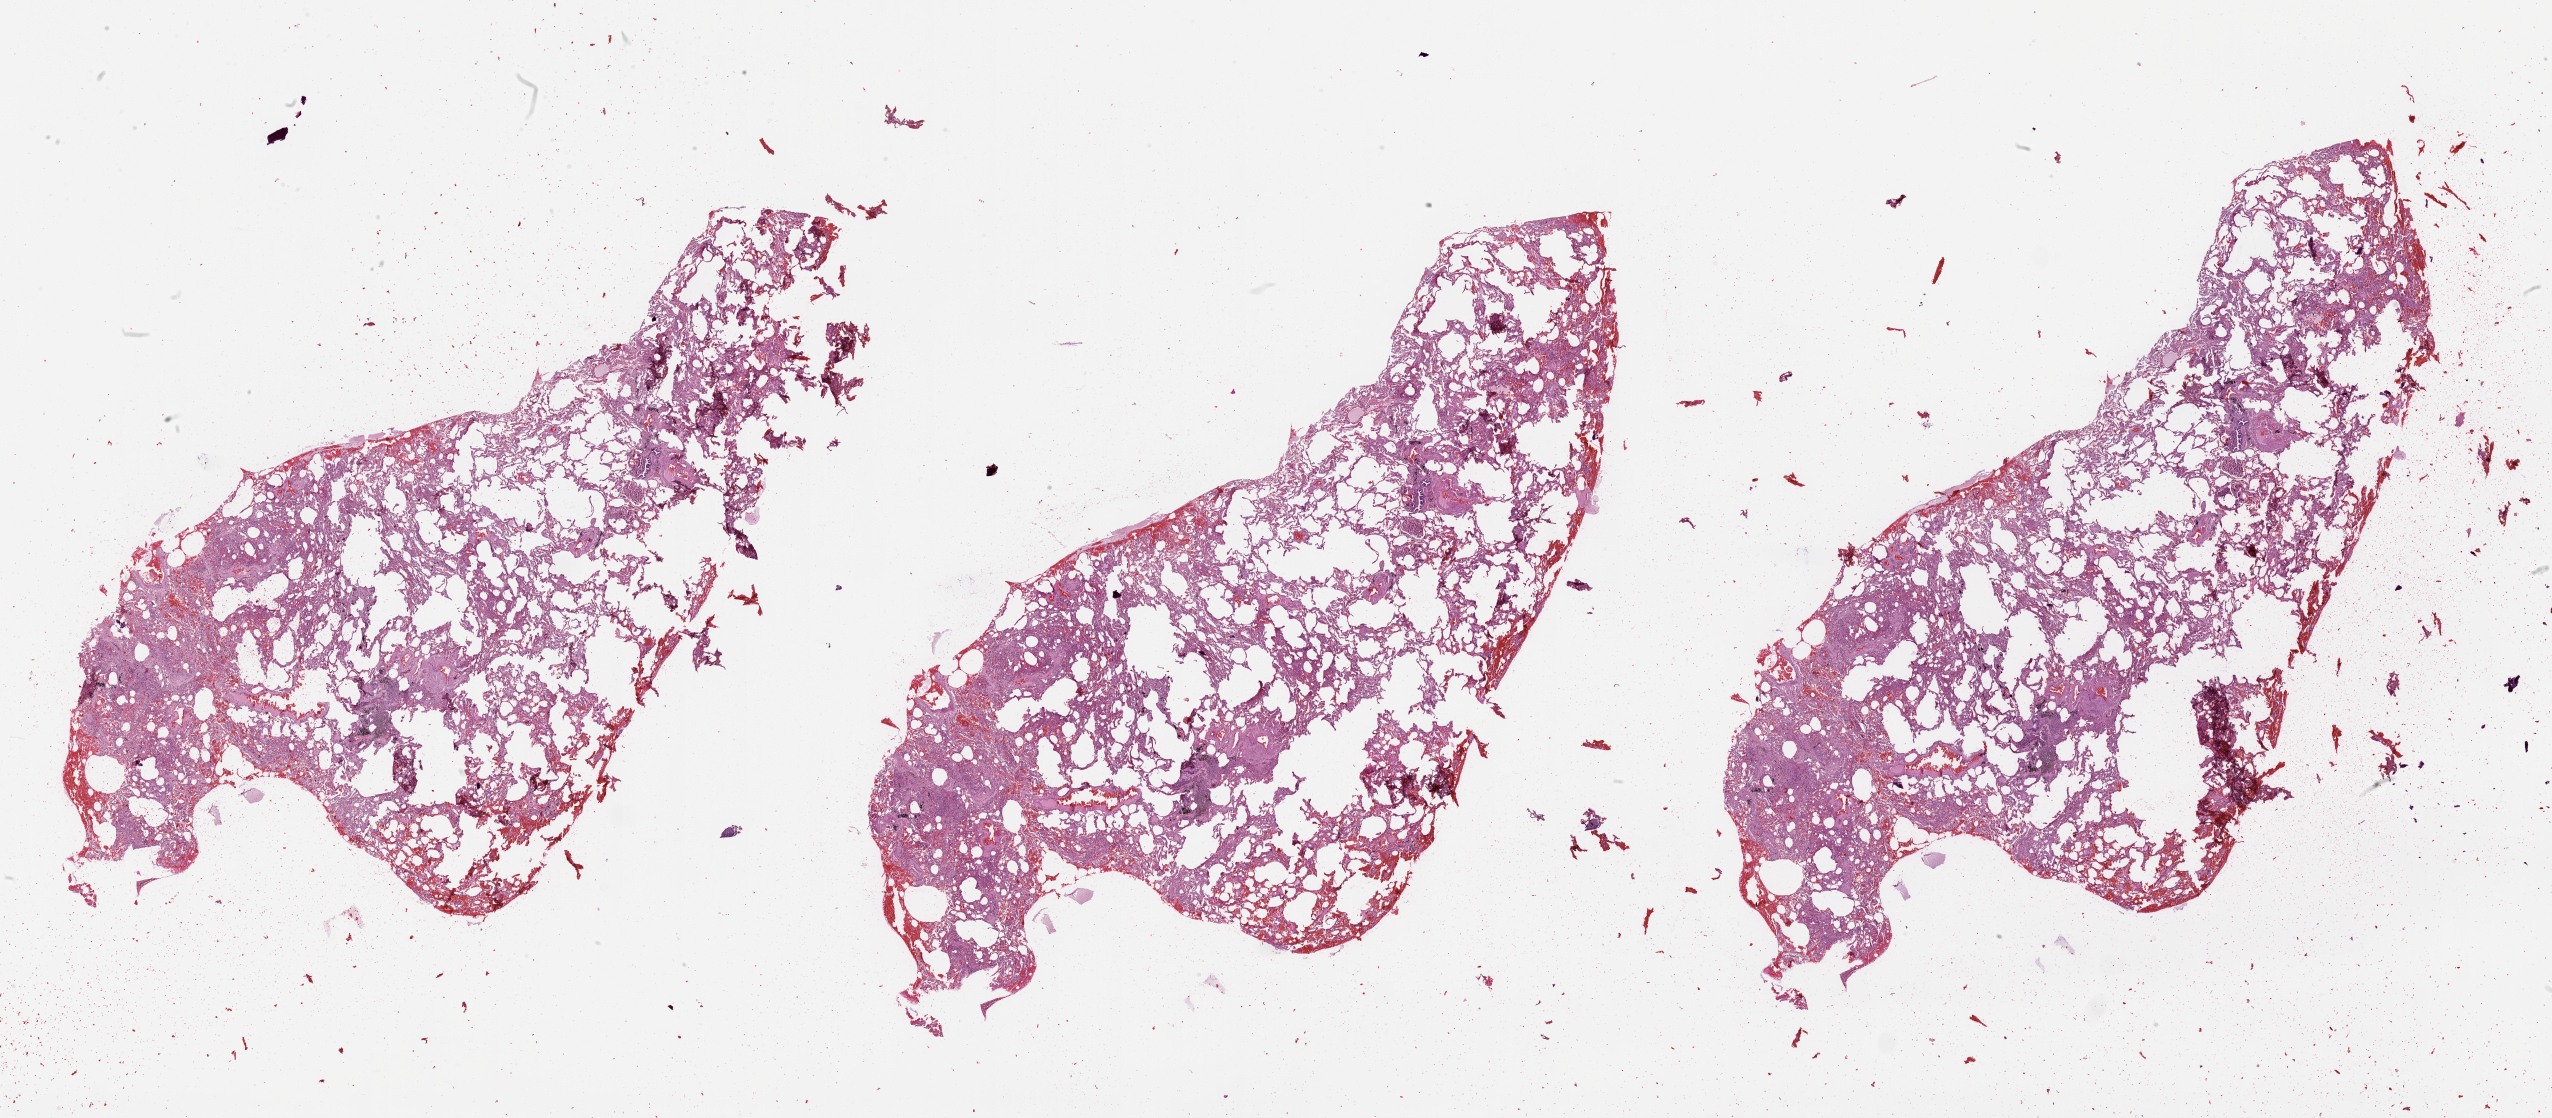
Whole-slide histology image, H&E-stained, a low-resolution overview of the entire scanned area, about 41.1 x 18.0 mm (from a 20x scan), lung, normal (non-tumour) tissue. Patient: male, age 58 years.
• this section: normal (non-tumour) tissue from the same patient
• patient diagnosis (cohort enrolment): squamous cell carcinoma (lung)